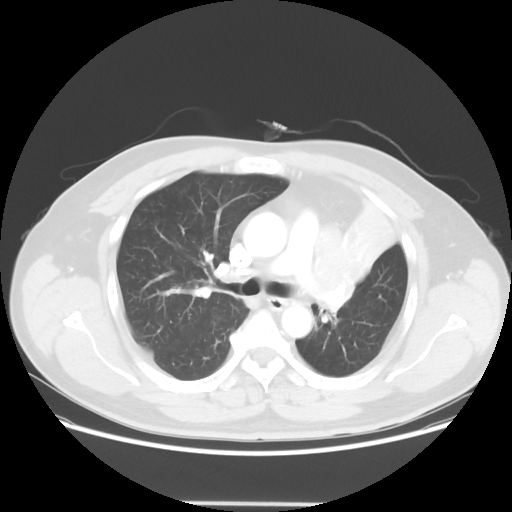
Chest CT, one axial slice; slice 40 of 62 in the series (ordered by position); reconstruction kernel STANDARD; 120 kVp; lung window (W 1500 / L -600 HU); 5 mm slice thickness; 512 × 512 image matrix, field of view 403 × 403 mm. Patient: male, 49 years. From the clinical record (not read from this slice): clinical TNM (as recorded): T3 N3 M1c.
Structures marked on this image (bounding box drawn by a radiologist):
- lung tumour (recorded histology: squamous cell carcinoma): box from (x=303, y=221) to (x=359, y=324) px